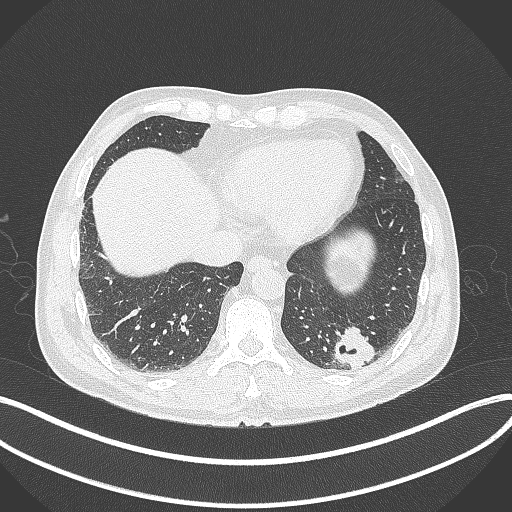
Chest CT, one axial slice; reconstruction kernel B70f; lung window (W 1500 / L -600 HU); 512 × 512 image matrix. Male patient, age 54 years. Case-level facts recorded for this patient, not image findings: clinical TNM (as recorded): T1c N0 M1.
Structures marked on this image (rectangle marked by the reading radiologist):
- lung tumour (recorded histology: adenocarcinoma): box from (x=330, y=325) to (x=376, y=373) px